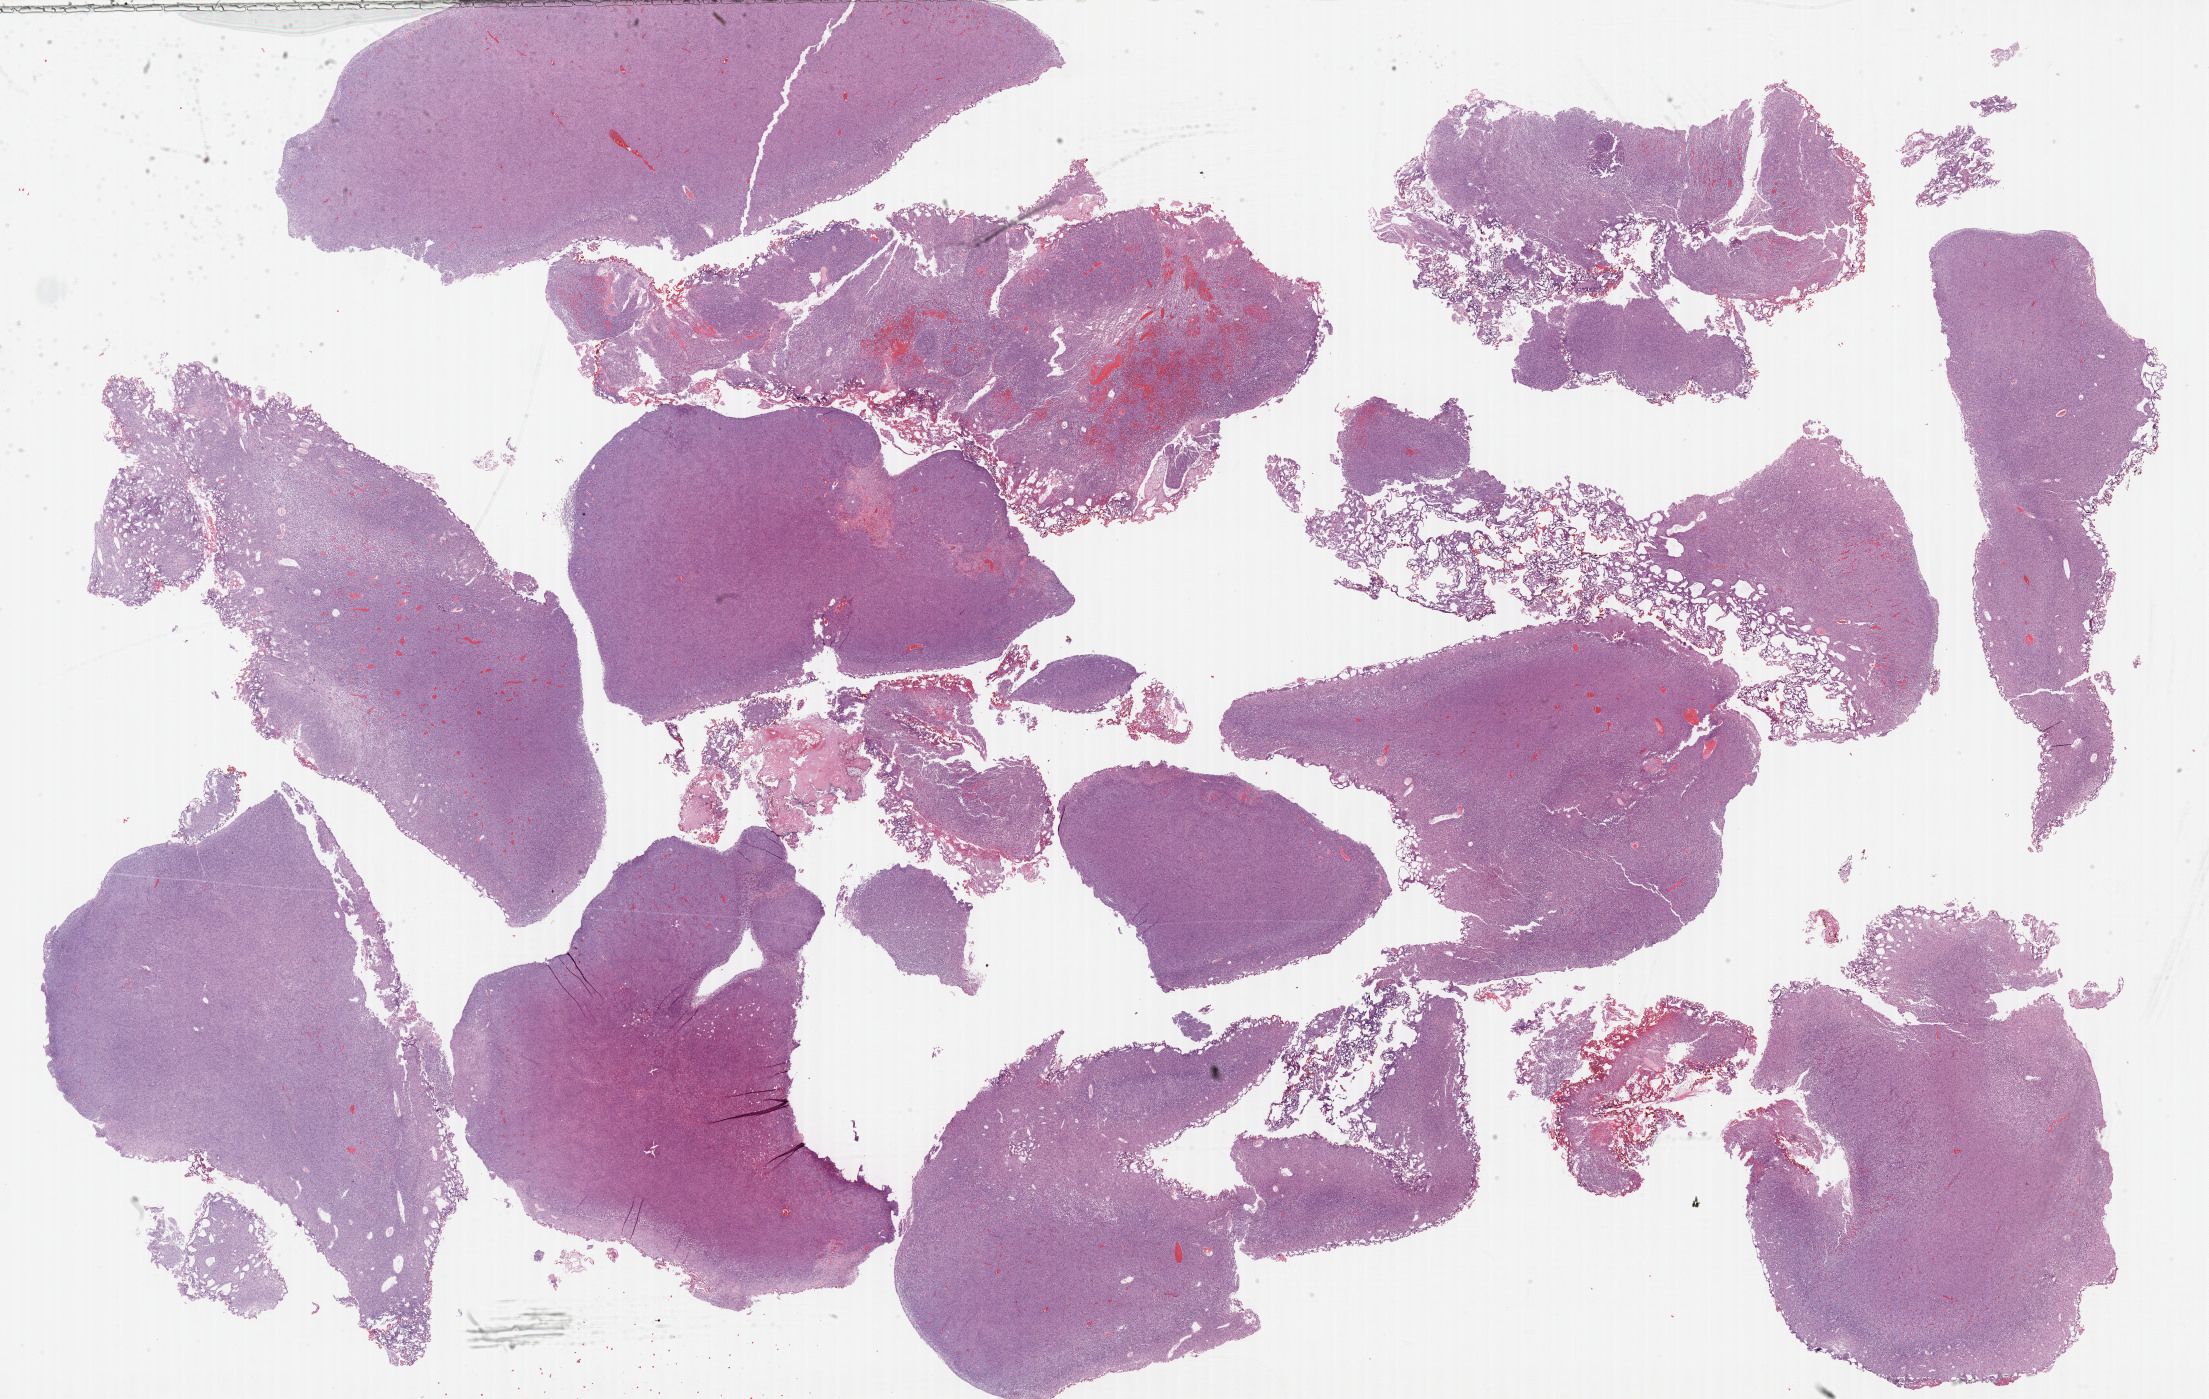
Whole-slide histology image, H&E-stained — low-resolution overview of the scanned area, about 35.7 x 22.6 mm; FFPE section; sample: primary tumour, bladder. Male, age 66 years at initial diagnosis. Histologic grade: high grade.
Pathologic diagnosis: Transitional cell carcinoma. TNM: T3b N1 M0. AJCC pathologic stage: IV (6th edition).